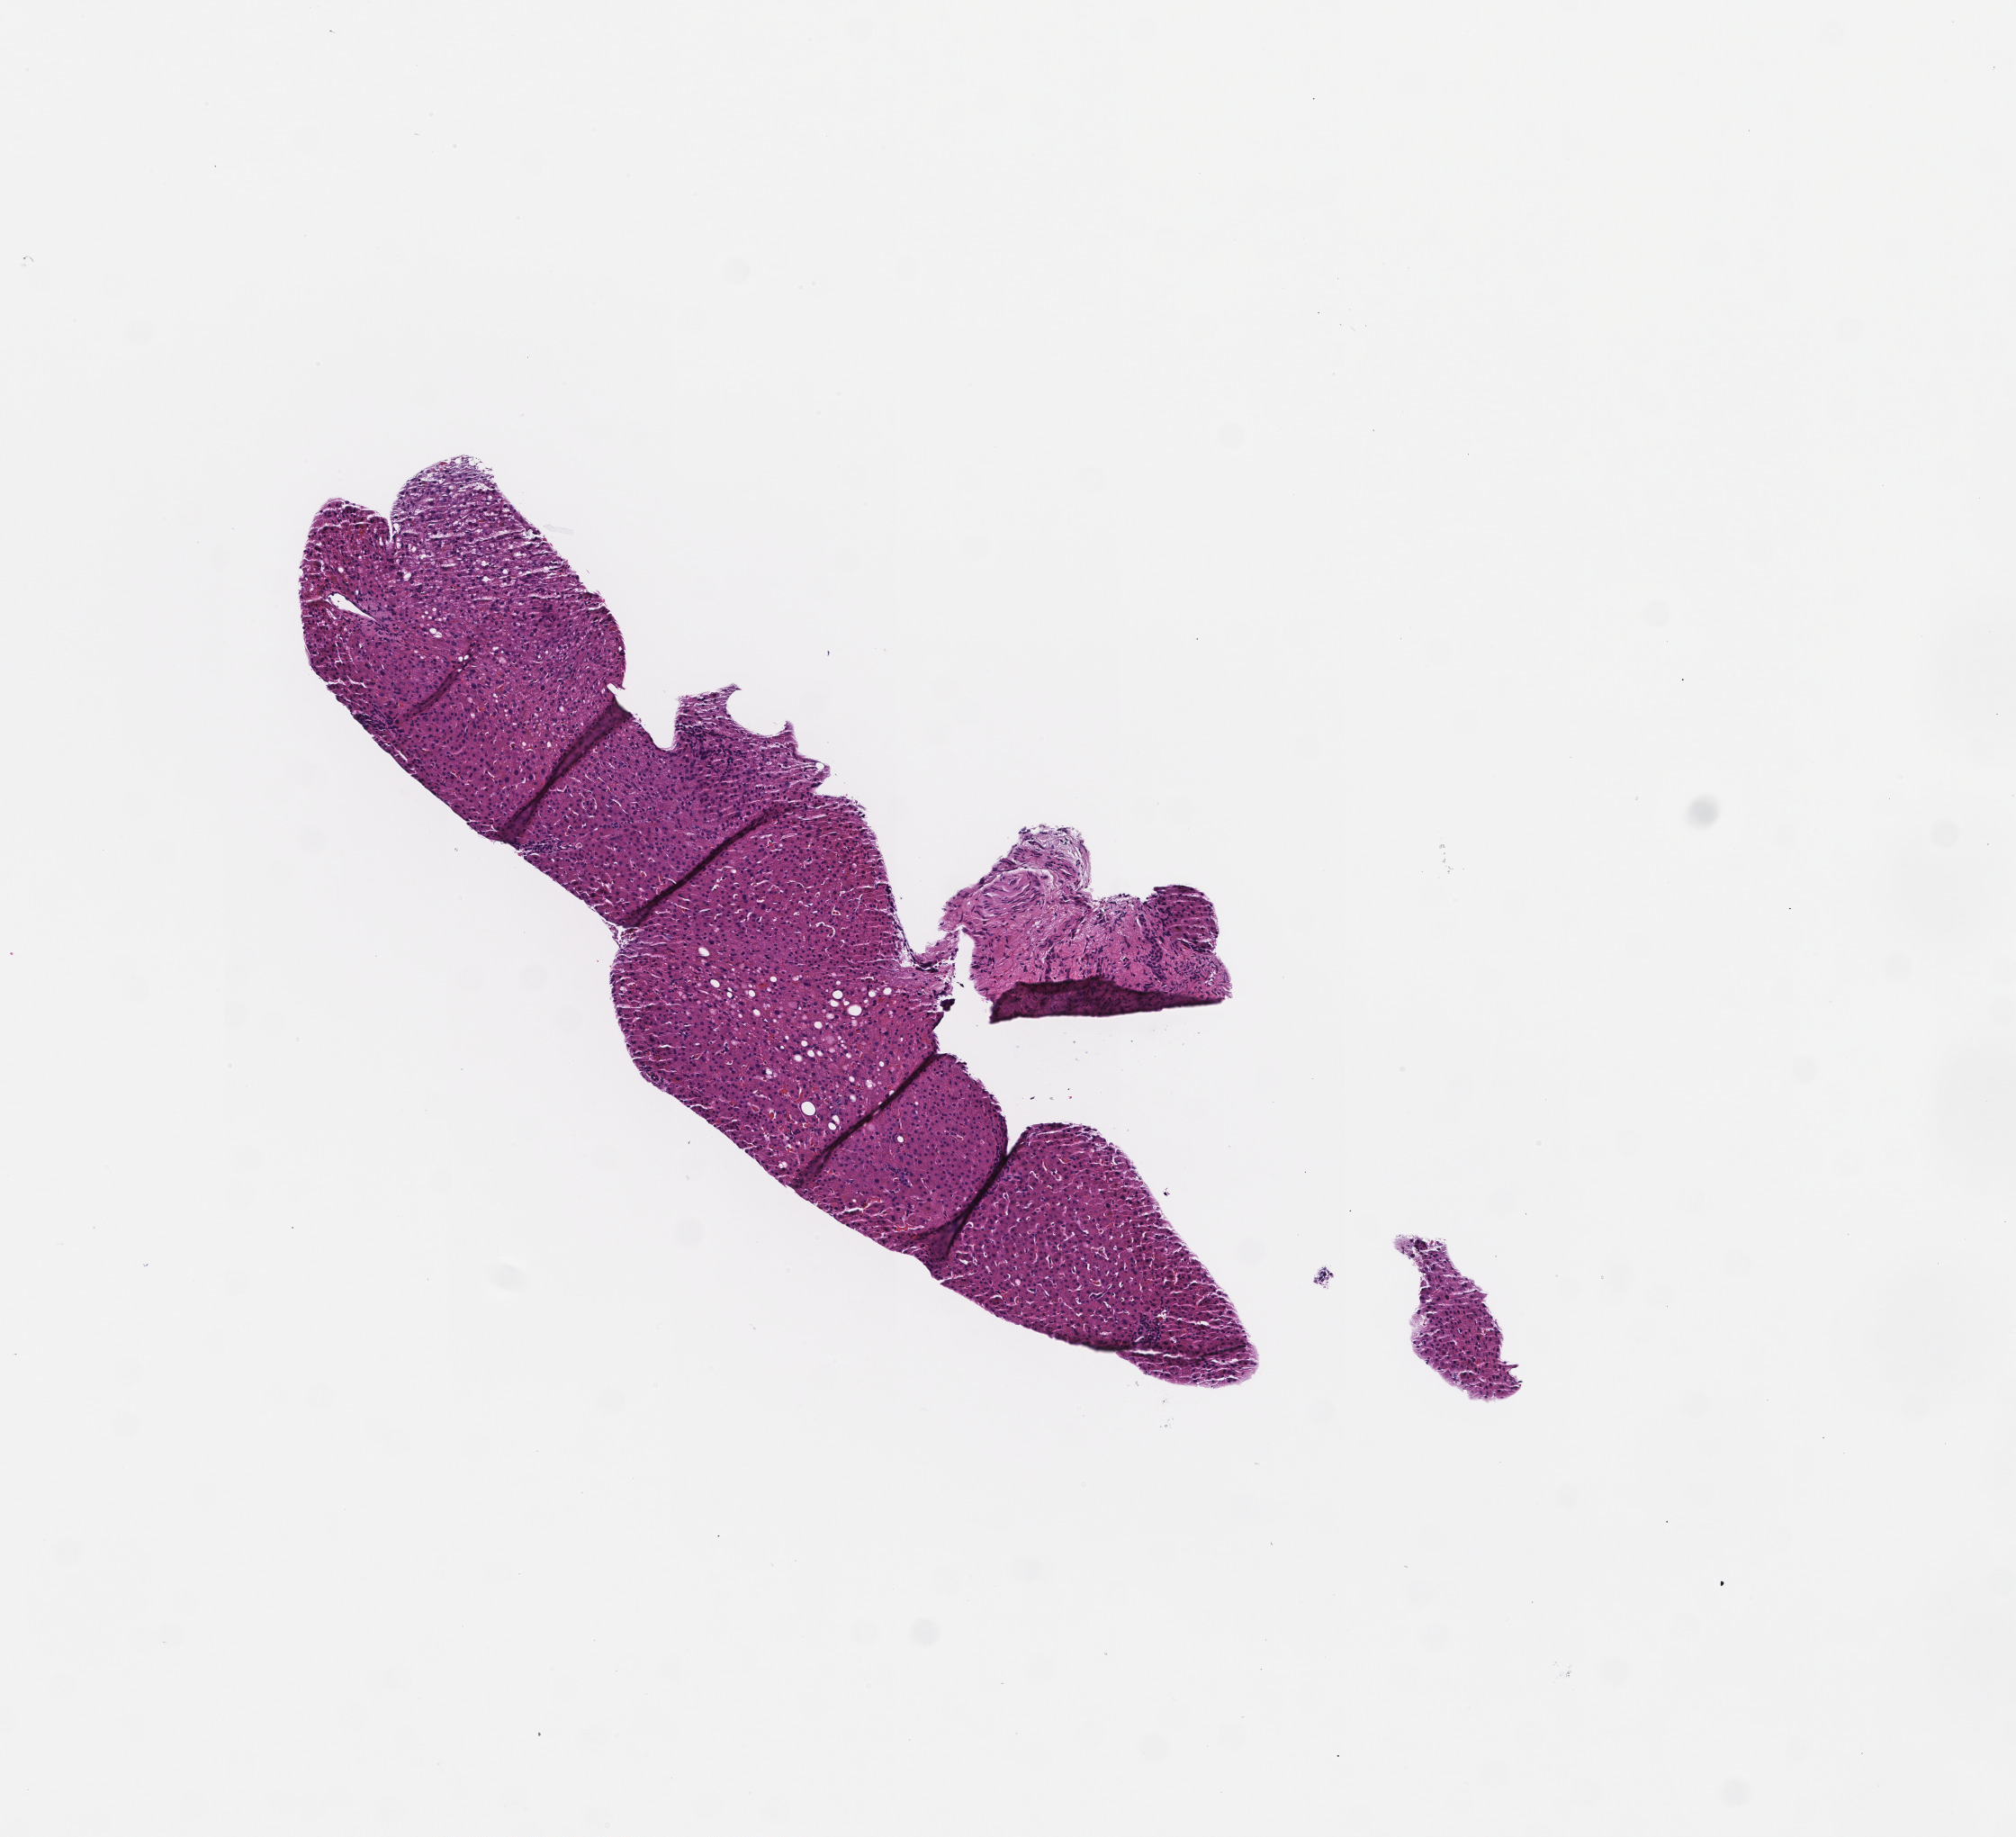
Digitized H&E-stained section, whole scanned area (about 4.5 x 4.1 mm) shown as a low-resolution overview, formalin-fixed, paraffin-embedded (FFPE) tissue, collected at baseline (before treatment). Patient: female.
- this section: metastasis (sampled organ not recorded)
- primary diagnosis of the patient: Non-Small Cell Lung Carcinoma